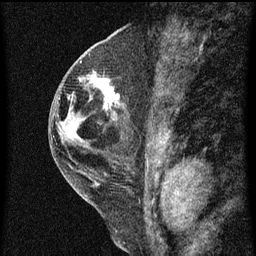
Breast MRI (dynamic contrast-enhanced), one sagittal slice; slice 28 of 60 in the series (ordered by position); dynamic contrast-enhanced series, image 2 of 3 at this slice position (ordered by acquisition); 1.5 T; TE 4.2 ms, TR 8 ms; 2 mm slice thickness; 256 × 256 image matrix, field of view 180 × 180 mm. Female patient, age 48 years.
Annotated regions visible in this slice (semi-automatic segmentation, software-assisted and operator-edited):
- analysis volume of interest (the breast-tissue region the enhancement analysis was run in; not a lesion): box from (x=89, y=72) to (x=123, y=113) px
- tumour enhancement mask (voxels above the 70 % enhancement threshold inside the analysis volume of interest): (x=93, y=78)–(x=120, y=109)